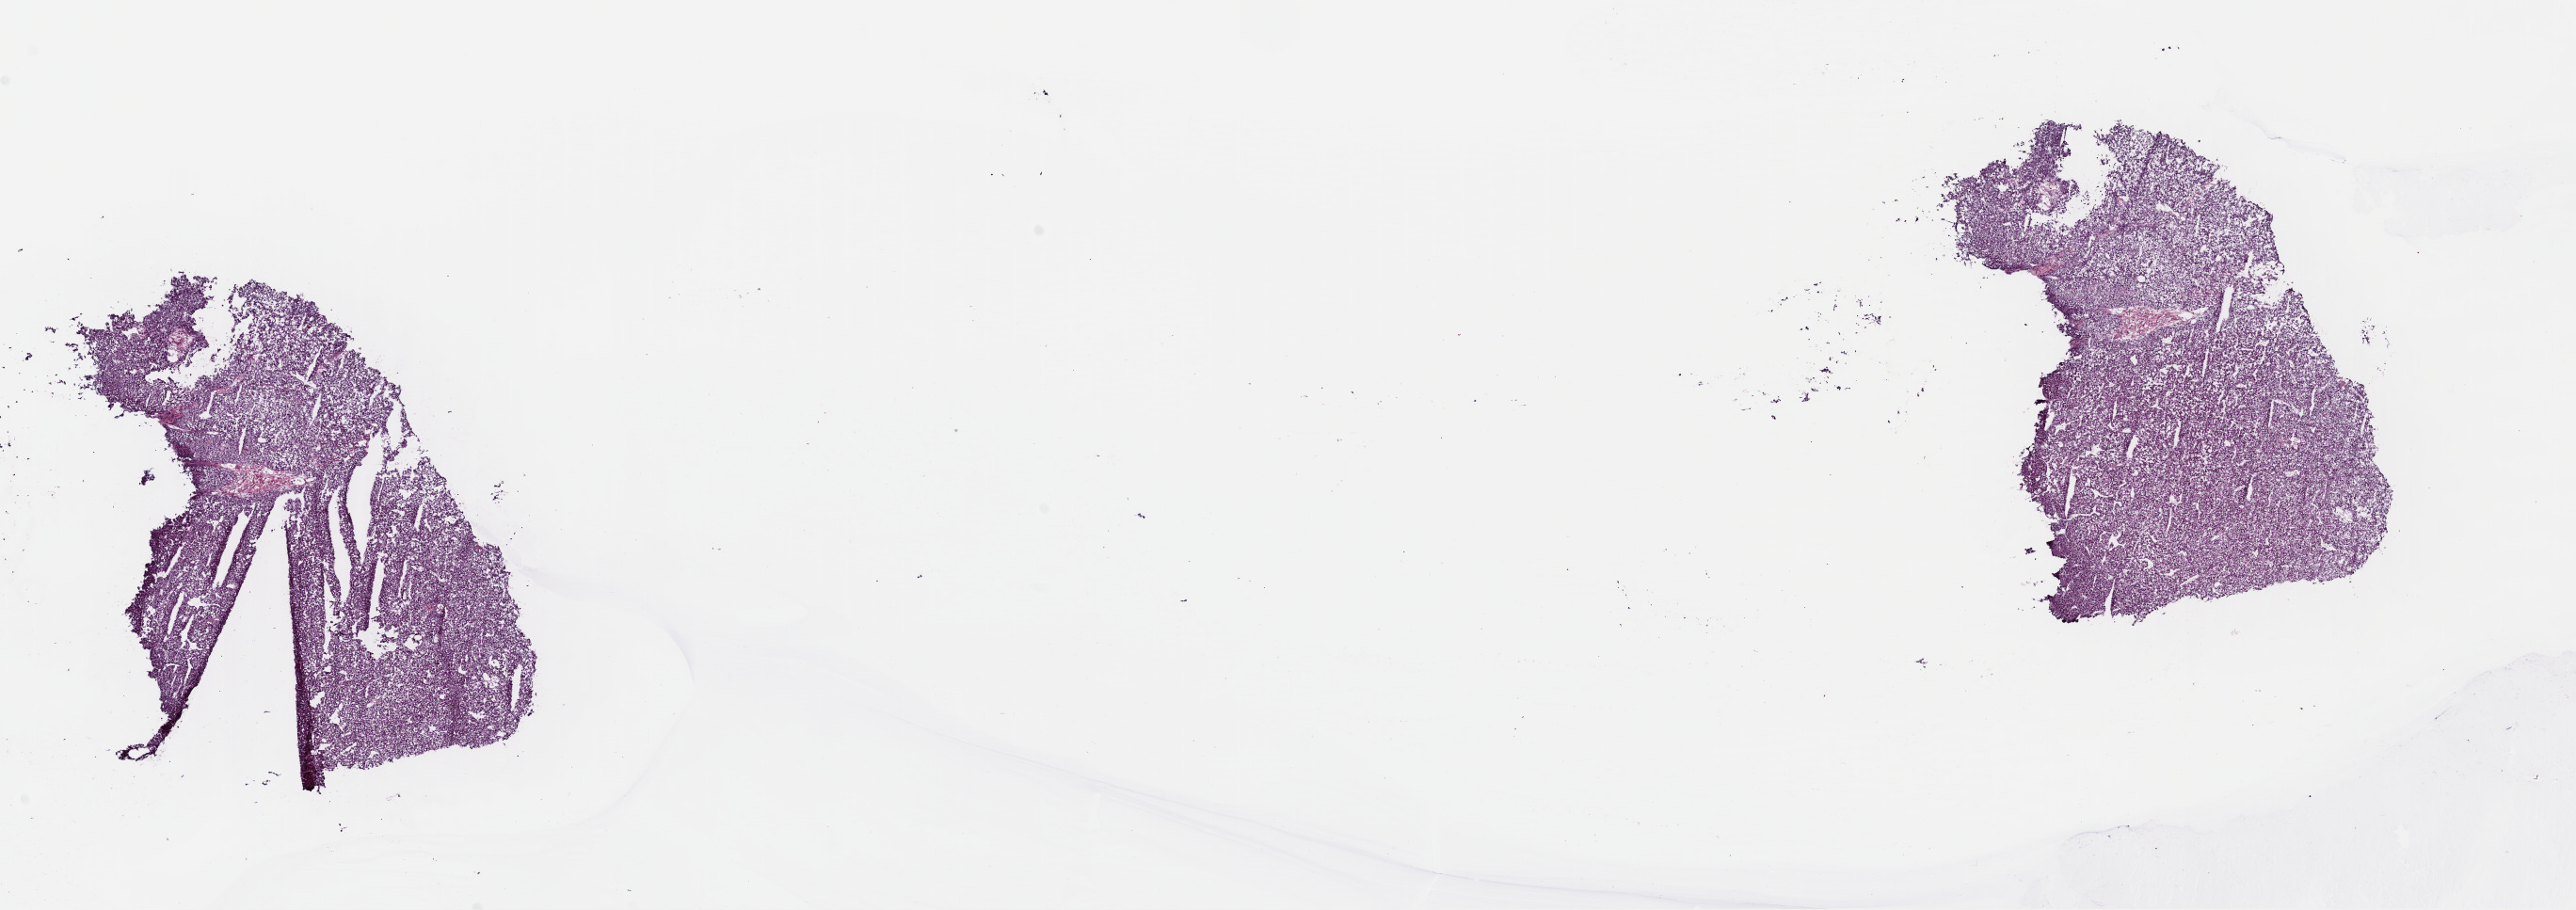
Digitized H&E tissue section (whole slide), whole scanned area (about 21.5 x 7.6 mm, slide scanned at 40x) shown as a low-resolution overview. Frozen section. Sample: primary tumour, adrenal cortex. Male, age 60 years at initial diagnosis. Composition of this section per pathologist review: tumour cells 95%, tumour nuclei 100%, normal cells 0%, stromal cells 4%, necrosis 1%. Infiltration values recorded for this section: lymphocyte infiltration 1%, monocyte infiltration 1%, neutrophil infiltration 0%.
- histologic diagnosis: Adrenal cortical carcinoma (cortex of adrenal gland)